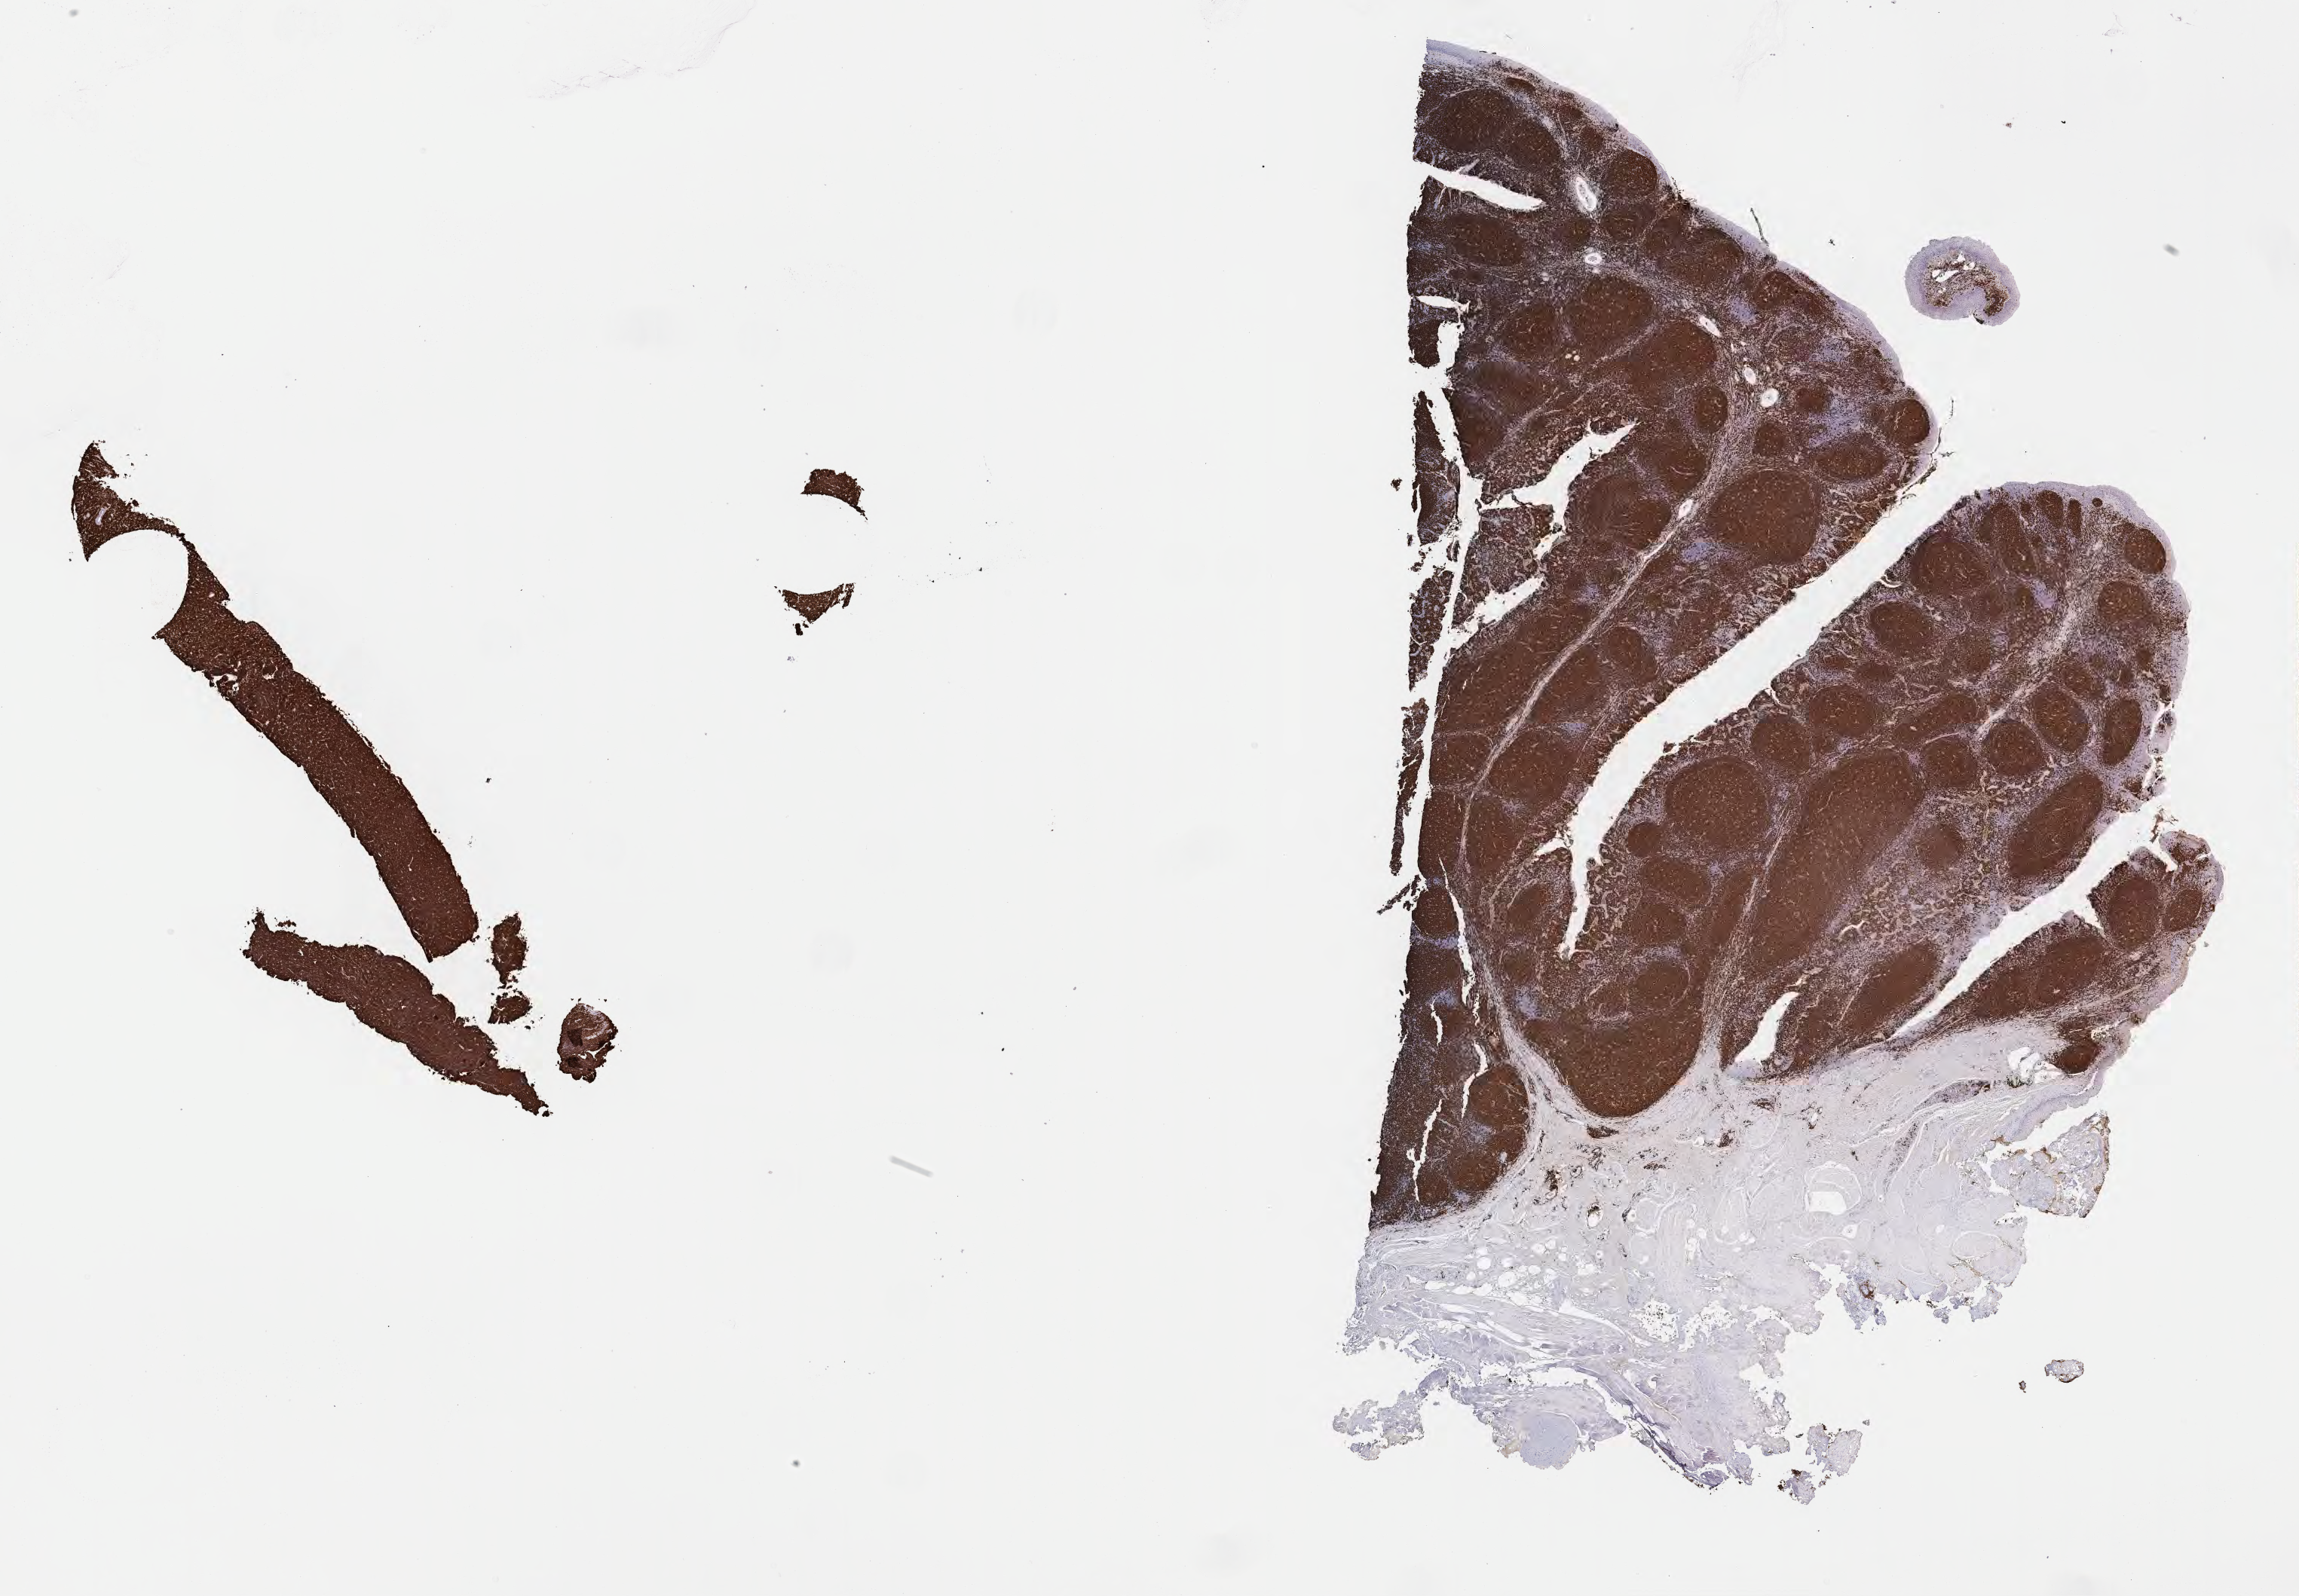
Immunohistochemistry (IHC) whole-slide image stained for CD20, a low-resolution overview of the entire scanned area, about 24.7 x 17.1 mm; specimen: tumor tissue; anatomic site: liver. Patient male; aged 15.
- diagnosis: Burkitt lymphoma, NOS